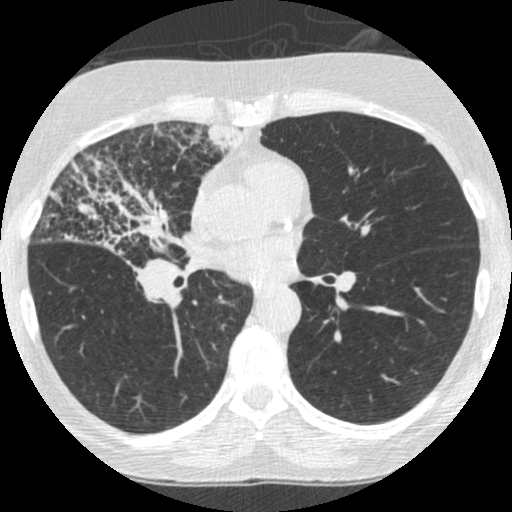
Low-dose screening chest CT, one axial slice. Reconstruction kernel STANDARD. 120 kVp. Lung window (W 1500 / L -600 HU). 1.25 mm slice thickness. 512 × 512 image matrix.
Structures marked on this image (manually delineated by an expert):
- lesion 2 (tumor, hilum of right lung): box from (x=45, y=150) to (x=193, y=267) px
- lesion 4 (tumor, upper lobe of right lung): (x=205, y=123)–(x=249, y=161)